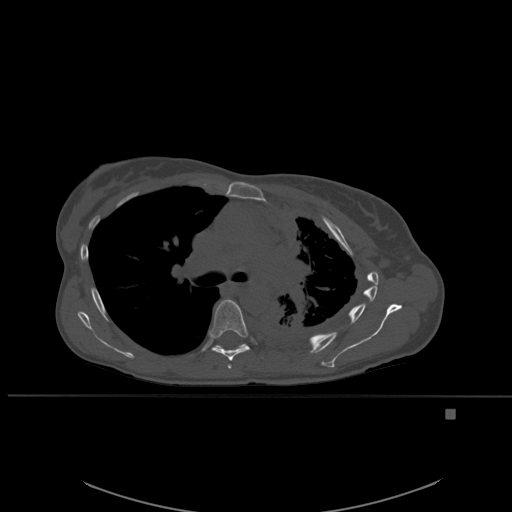
CT including the spine, one axial slice. Bone window (W 1800 / L 400 HU). 512 × 512 image matrix. Female patient, age 45 years. From the clinical record (not read from this slice): primary cancer: lung.
Annotated regions visible in this slice (semi-automatic segmentation, software-assisted and operator-edited):
- T5 vertebra: bounding box <227,364,232,369> (left, top, right, bottom; pixels)
- T6 vertebra: <209,299,250,361>
- T7 vertebra: <215,344,246,349>